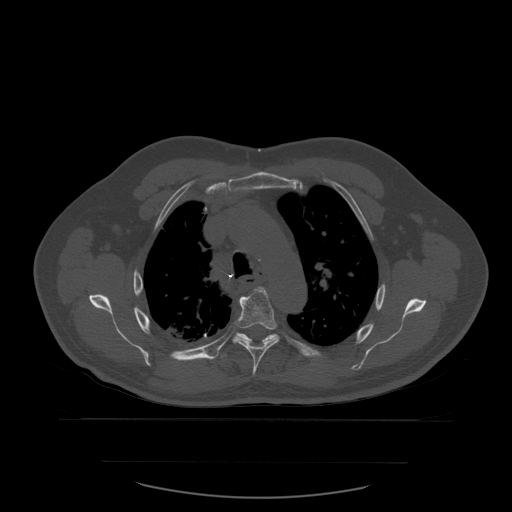
CT including the spine, one axial slice; slice 421 of 590 in the series (ordered by position); bone window (W 1800 / L 400 HU); 1.25 mm slice thickness; 512 × 512 image matrix. Patient age 71 years. Case-level facts recorded for this patient, not image findings: primary cancer: lung; vertebrae with lytic lesions (as recorded): T1, T2, L5, S1.
Annotated regions visible in this slice (semi-automatically segmented with operator editing):
- T5 vertebra: bounding box (x1, y1, x2, y2) in pixels: (233, 288, 280, 376)
- T6 vertebra: (226, 333, 278, 357)